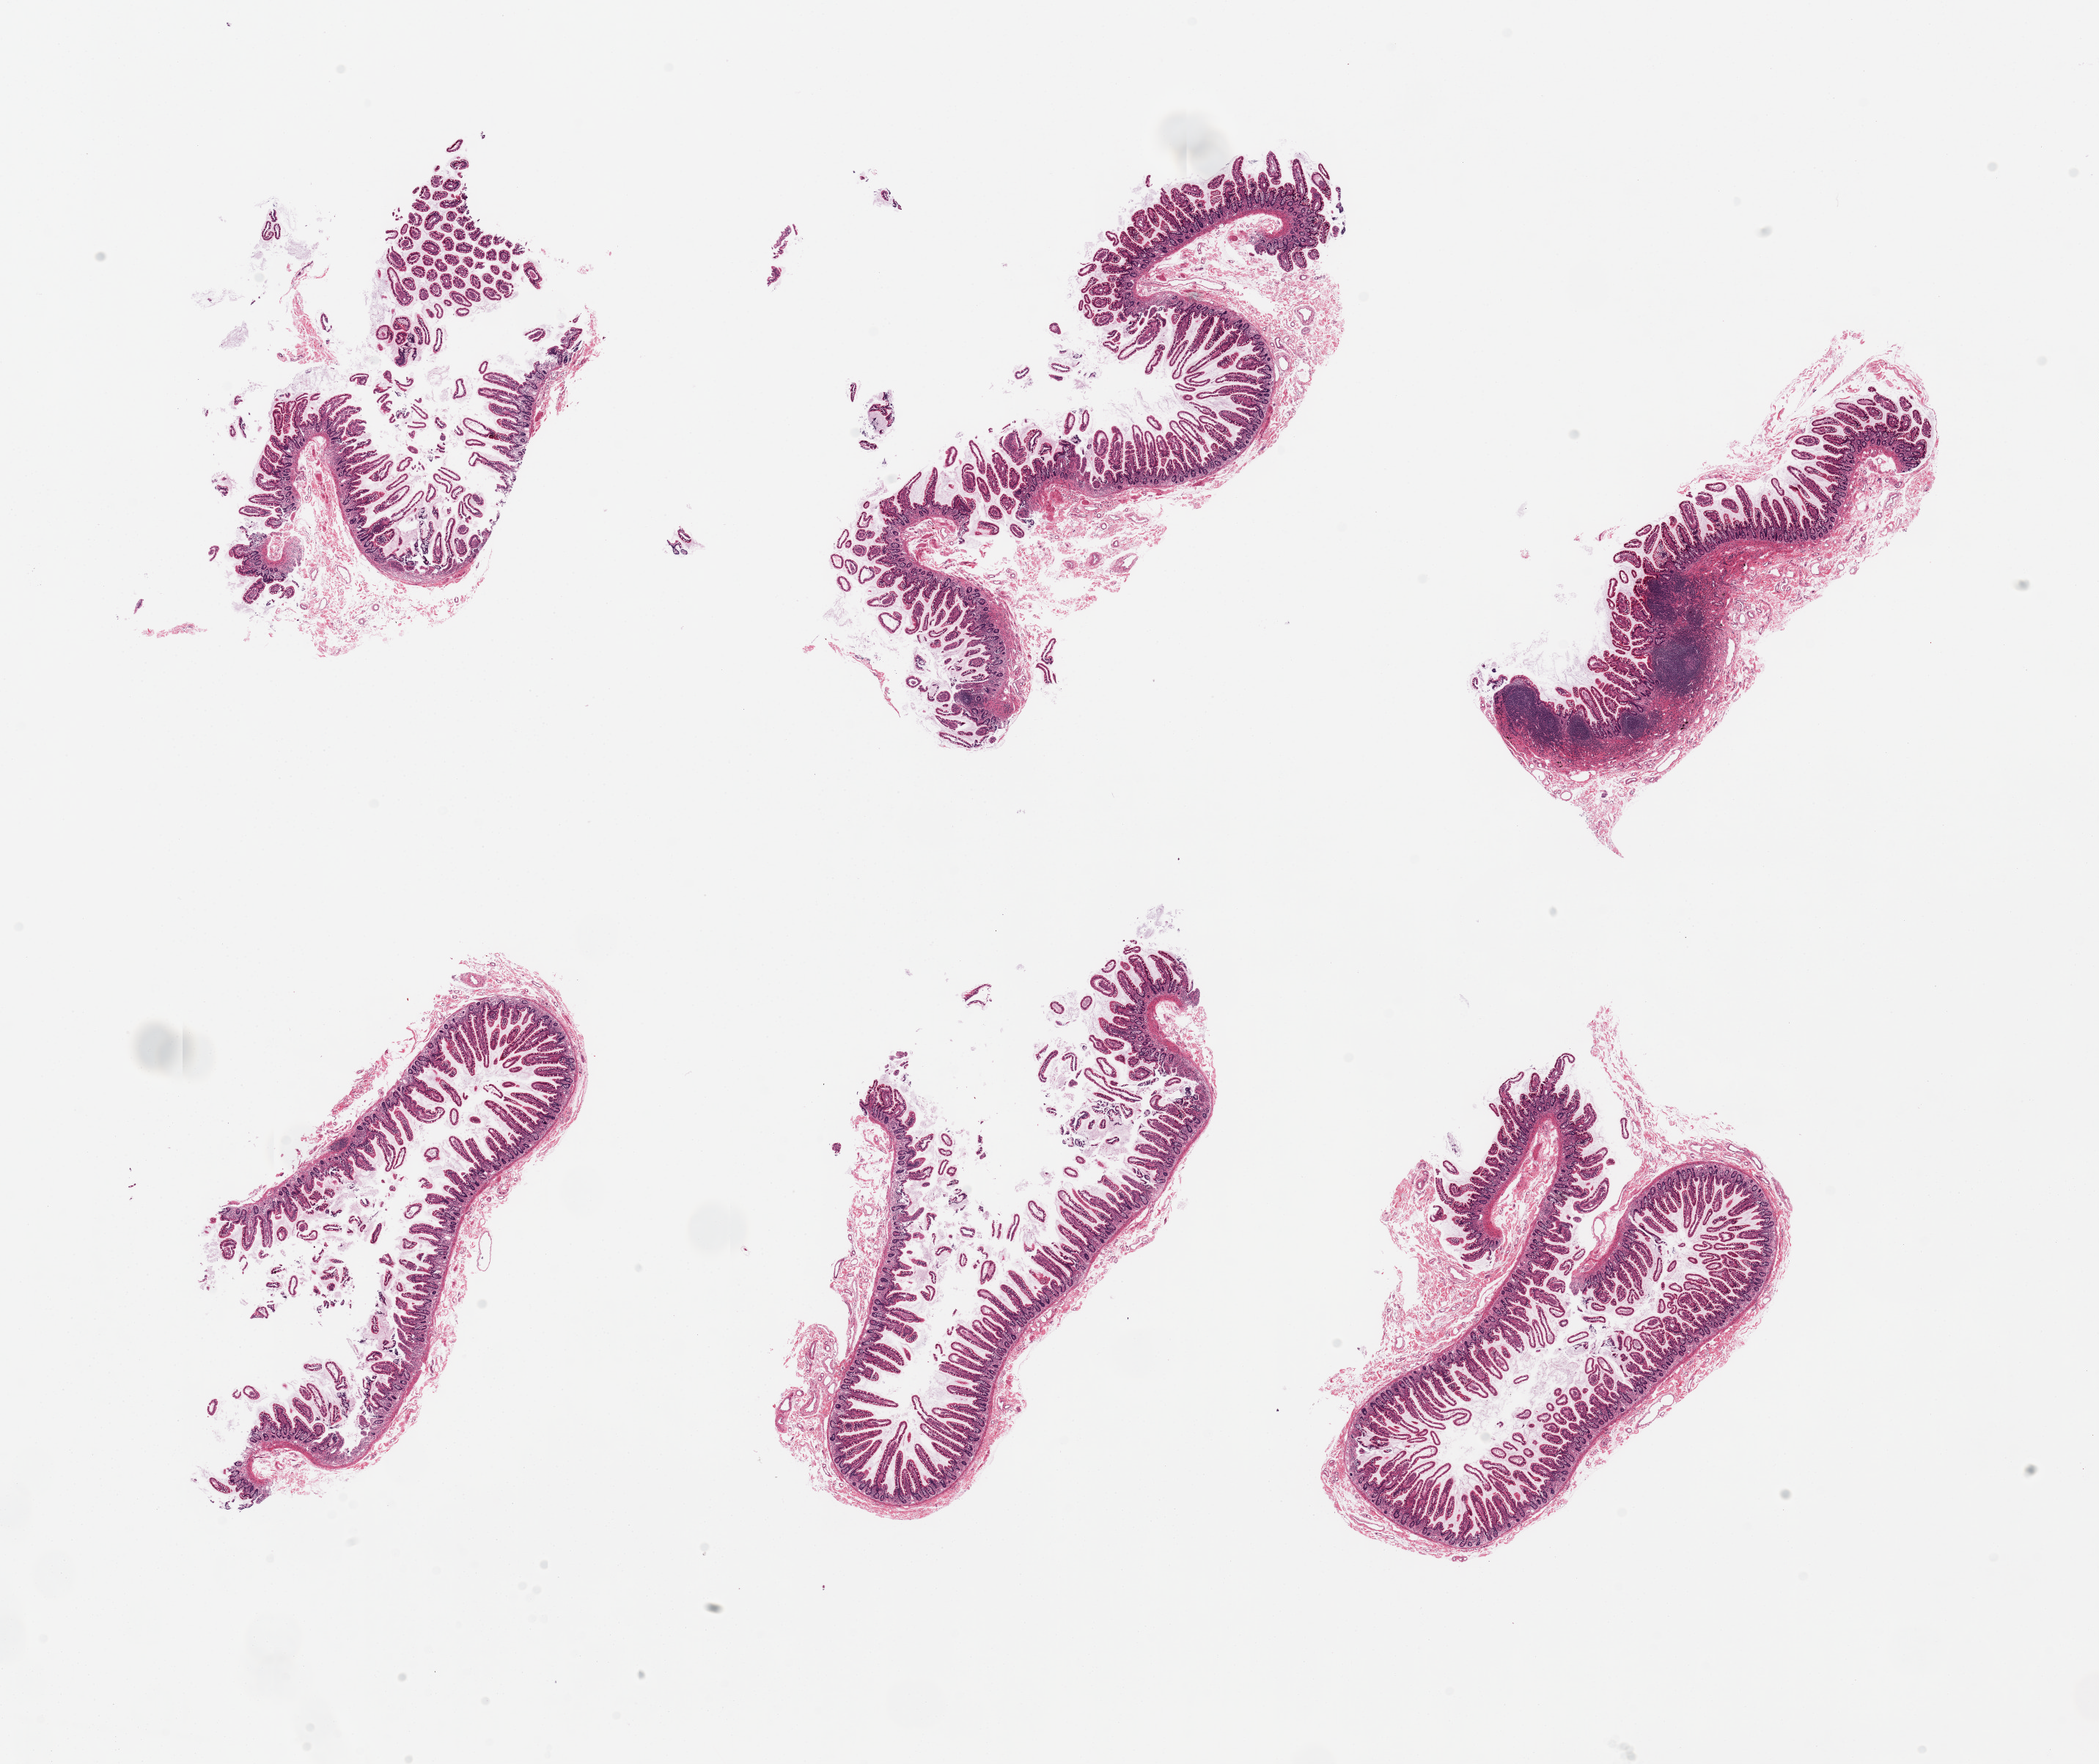
H&E whole-slide image — shown as a low-resolution overview of the whole scanned area (about 22.6 x 19.0 mm, slide scanned at 20x), PAXgene-fixed, paraffin-embedded tissue, sampled site (target tissue): ileum, tissue donor sample. Donor: female.
Review note (as recorded): 6 pieces, fragmented mucosa with only minimal lymphoid tissue.